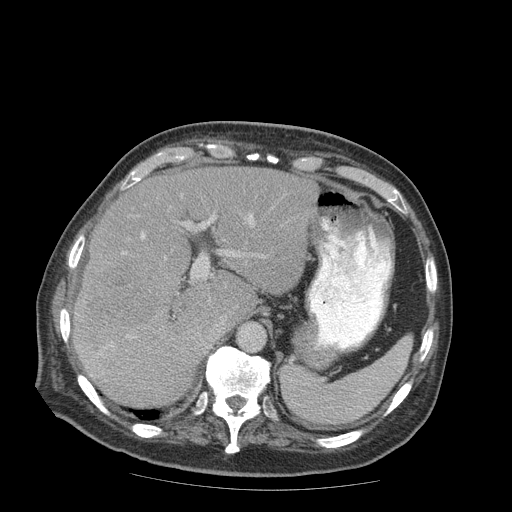
Contrast-enhanced abdominal CT (liver protocol), one axial slice; position 61 of 99 along the scan axis; soft-tissue window (W 400 / L 40 HU); 512 × 512 image matrix. From the clinical record (not read from this slice): diagnosis: hepatocellular carcinoma (patient treated with transarterial chemoembolisation; whether this scan precedes or follows treatment is not stated here); TNM stage (as recorded): Stage-IIIB; Child-Pugh class: A.
Annotated regions visible in this slice (semi-automatic segmentation, software-assisted and operator-edited):
- liver parenchyma outside the tumour (the mass and vessels are separate outlines, so this box may not span the whole liver): bounding box [x1, y1, x2, y2] px = [72, 168, 316, 406]
- mass: [74, 257, 158, 350]
- liver vessels: [91, 214, 254, 376]